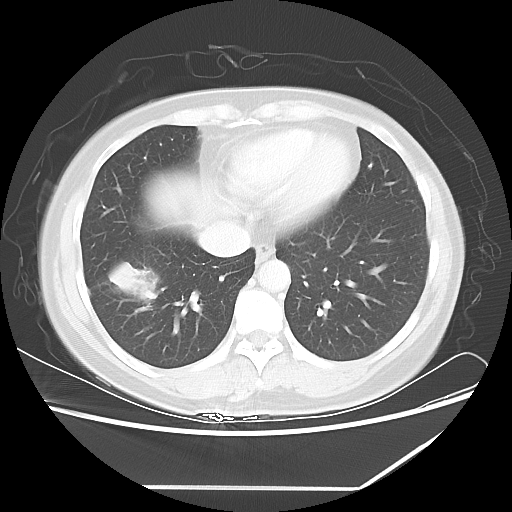
Chest CT, one axial slice; slice 21 of 60 in the series (ordered by position); 100 kVp; lung window (W 1500 / L -600 HU); 5 mm slice thickness; 512 × 512 image matrix, field of view 374 × 374 mm. Female patient, age 42 years. From the clinical record (not read from this slice): clinical TNM (as recorded): T2 N1 M0.
Annotated regions visible in this slice (rectangle marked by the reading radiologist):
- lung tumour (recorded histology: adenocarcinoma): box from (x=103, y=257) to (x=162, y=310) px